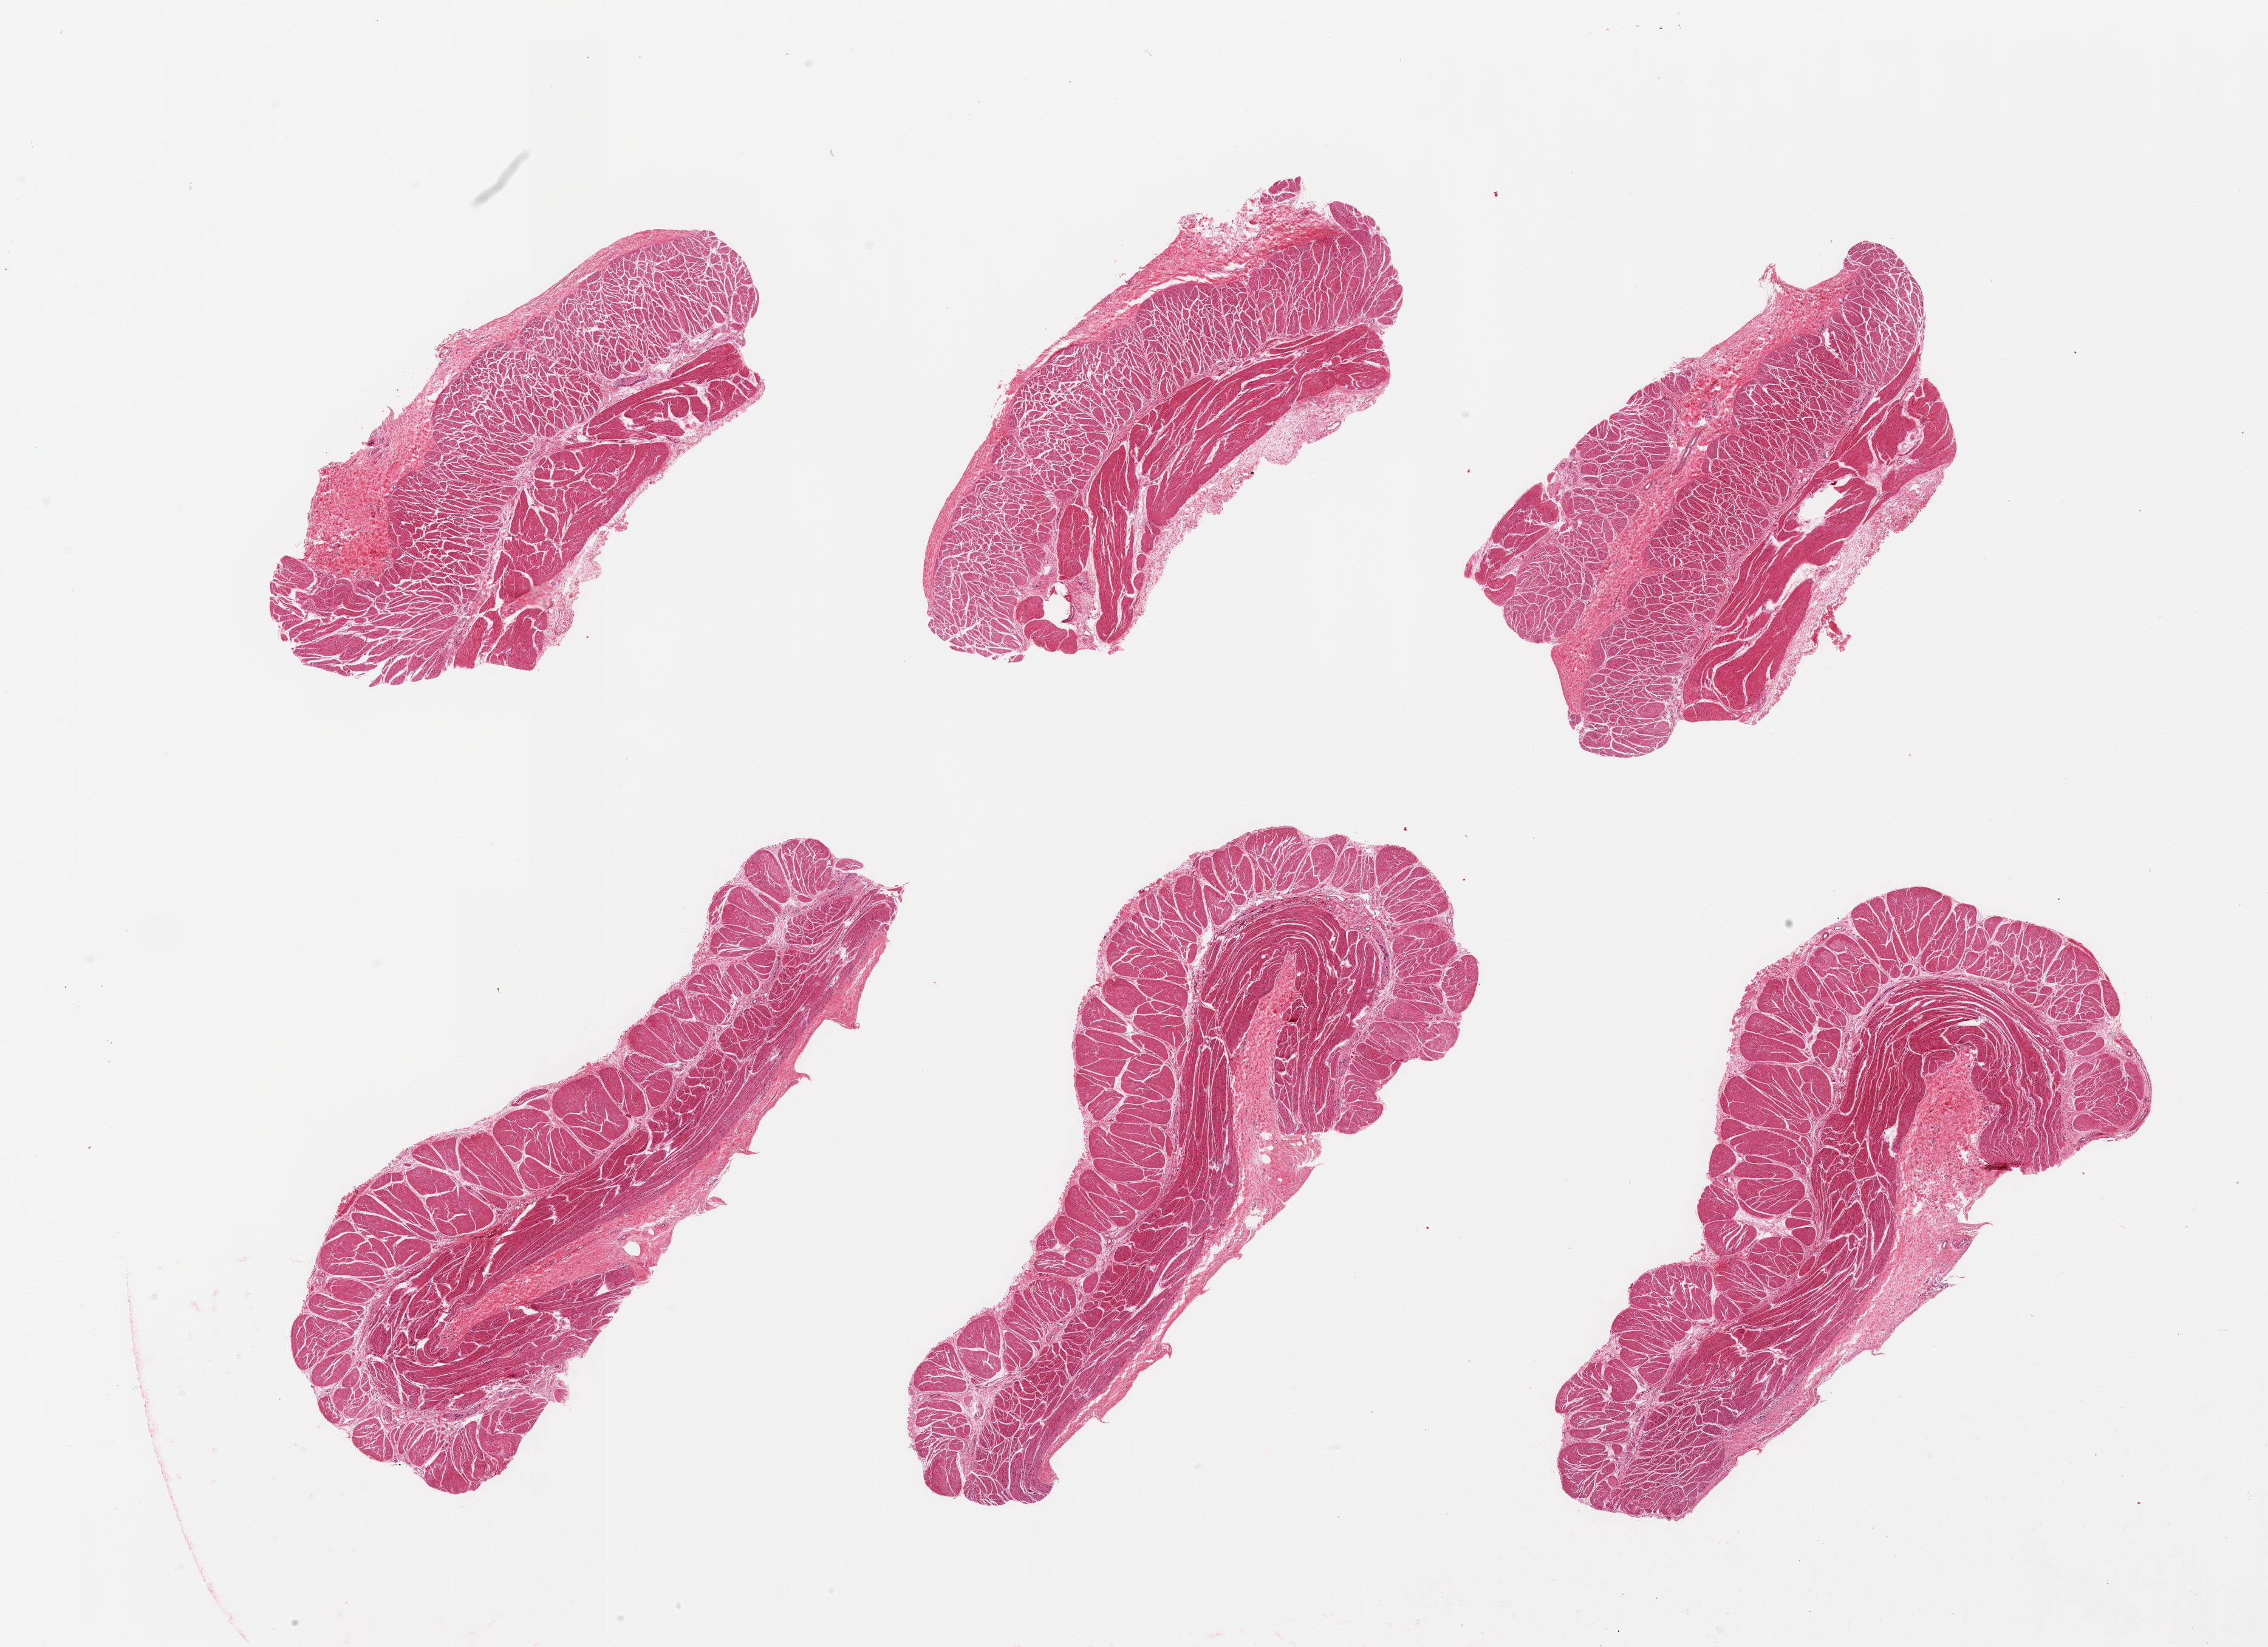
Digitized haematoxylin and eosin-stained section — low-resolution overview of the scanned area, about 29.5 x 21.4 mm (slide scanned at 20x); PAXgene-fixed, paraffin-embedded tissue; section of esophageal muscle (target tissue); tissue donor sample. Donor: female.
Pathologist's review note for this sample: 6 pieces; target muscularis.